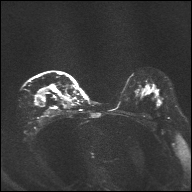
Breast MRI, one axial slice. Position 24 of 32 along the scan axis. Diffusion-weighted series; image 2 of 4 stored at this slice position (different b-values; order by instance number). 1.5 T. 4 mm slice thickness. 192 × 192 image matrix, field of view 360 × 360 mm. Female patient.
Annotated regions visible in this slice (manually delineated by an expert):
- tumour on diffusion-weighted imaging: box from (x=52, y=89) to (x=56, y=91) px